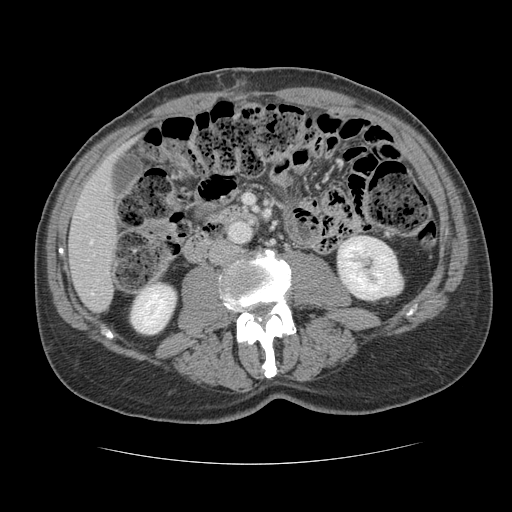
Contrast-enhanced abdominal CT, one axial slice. Slice 37 of 134 in the series (ordered by position). 120 kVp. Intravenous contrast given. Soft-tissue window (W 400 / L 40 HU). 512 × 512 image matrix, field of view 377 × 377 mm. Male patient, age 68 years. Case-level facts recorded for this patient, not image findings: diagnosis: colorectal cancer liver metastases, imaged before liver resection; multiple liver metastases: yes; largest metastasis: 2.2 cm; disease in both lobes: no.
Structures marked on this image (outlined manually by an expert reader):
- hepatic veins: bounding box [x1, y1, x2, y2] px = [90, 240, 93, 243]
- liver: [70, 164, 119, 311]
- planned liver remnant (the part of the liver to remain after resection): [70, 164, 118, 311]